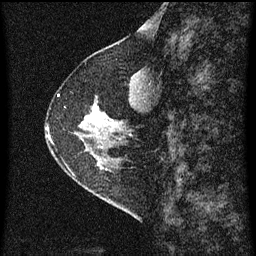
Breast MRI (dynamic contrast-enhanced), one sagittal slice; position 22 of 60 along the scan axis; dynamic contrast-enhanced series, image 2 of 3 at this slice position (ordered by acquisition); 1.5 T; TE 4.2 ms, TR 8 ms; 2 mm slice thickness; 256 × 256 image matrix, field of view 180 × 180 mm. Female patient, age 56 years.
Outlined on this slice (semi-automatic segmentation, software-assisted and operator-edited):
- analysis volume of interest (the breast-tissue region the enhancement analysis was run in; not a lesion): box from (x=49, y=96) to (x=110, y=159) px
- tumour enhancement mask (voxels above the 70 % enhancement threshold inside the analysis volume of interest): (x=85, y=108)–(x=108, y=123)